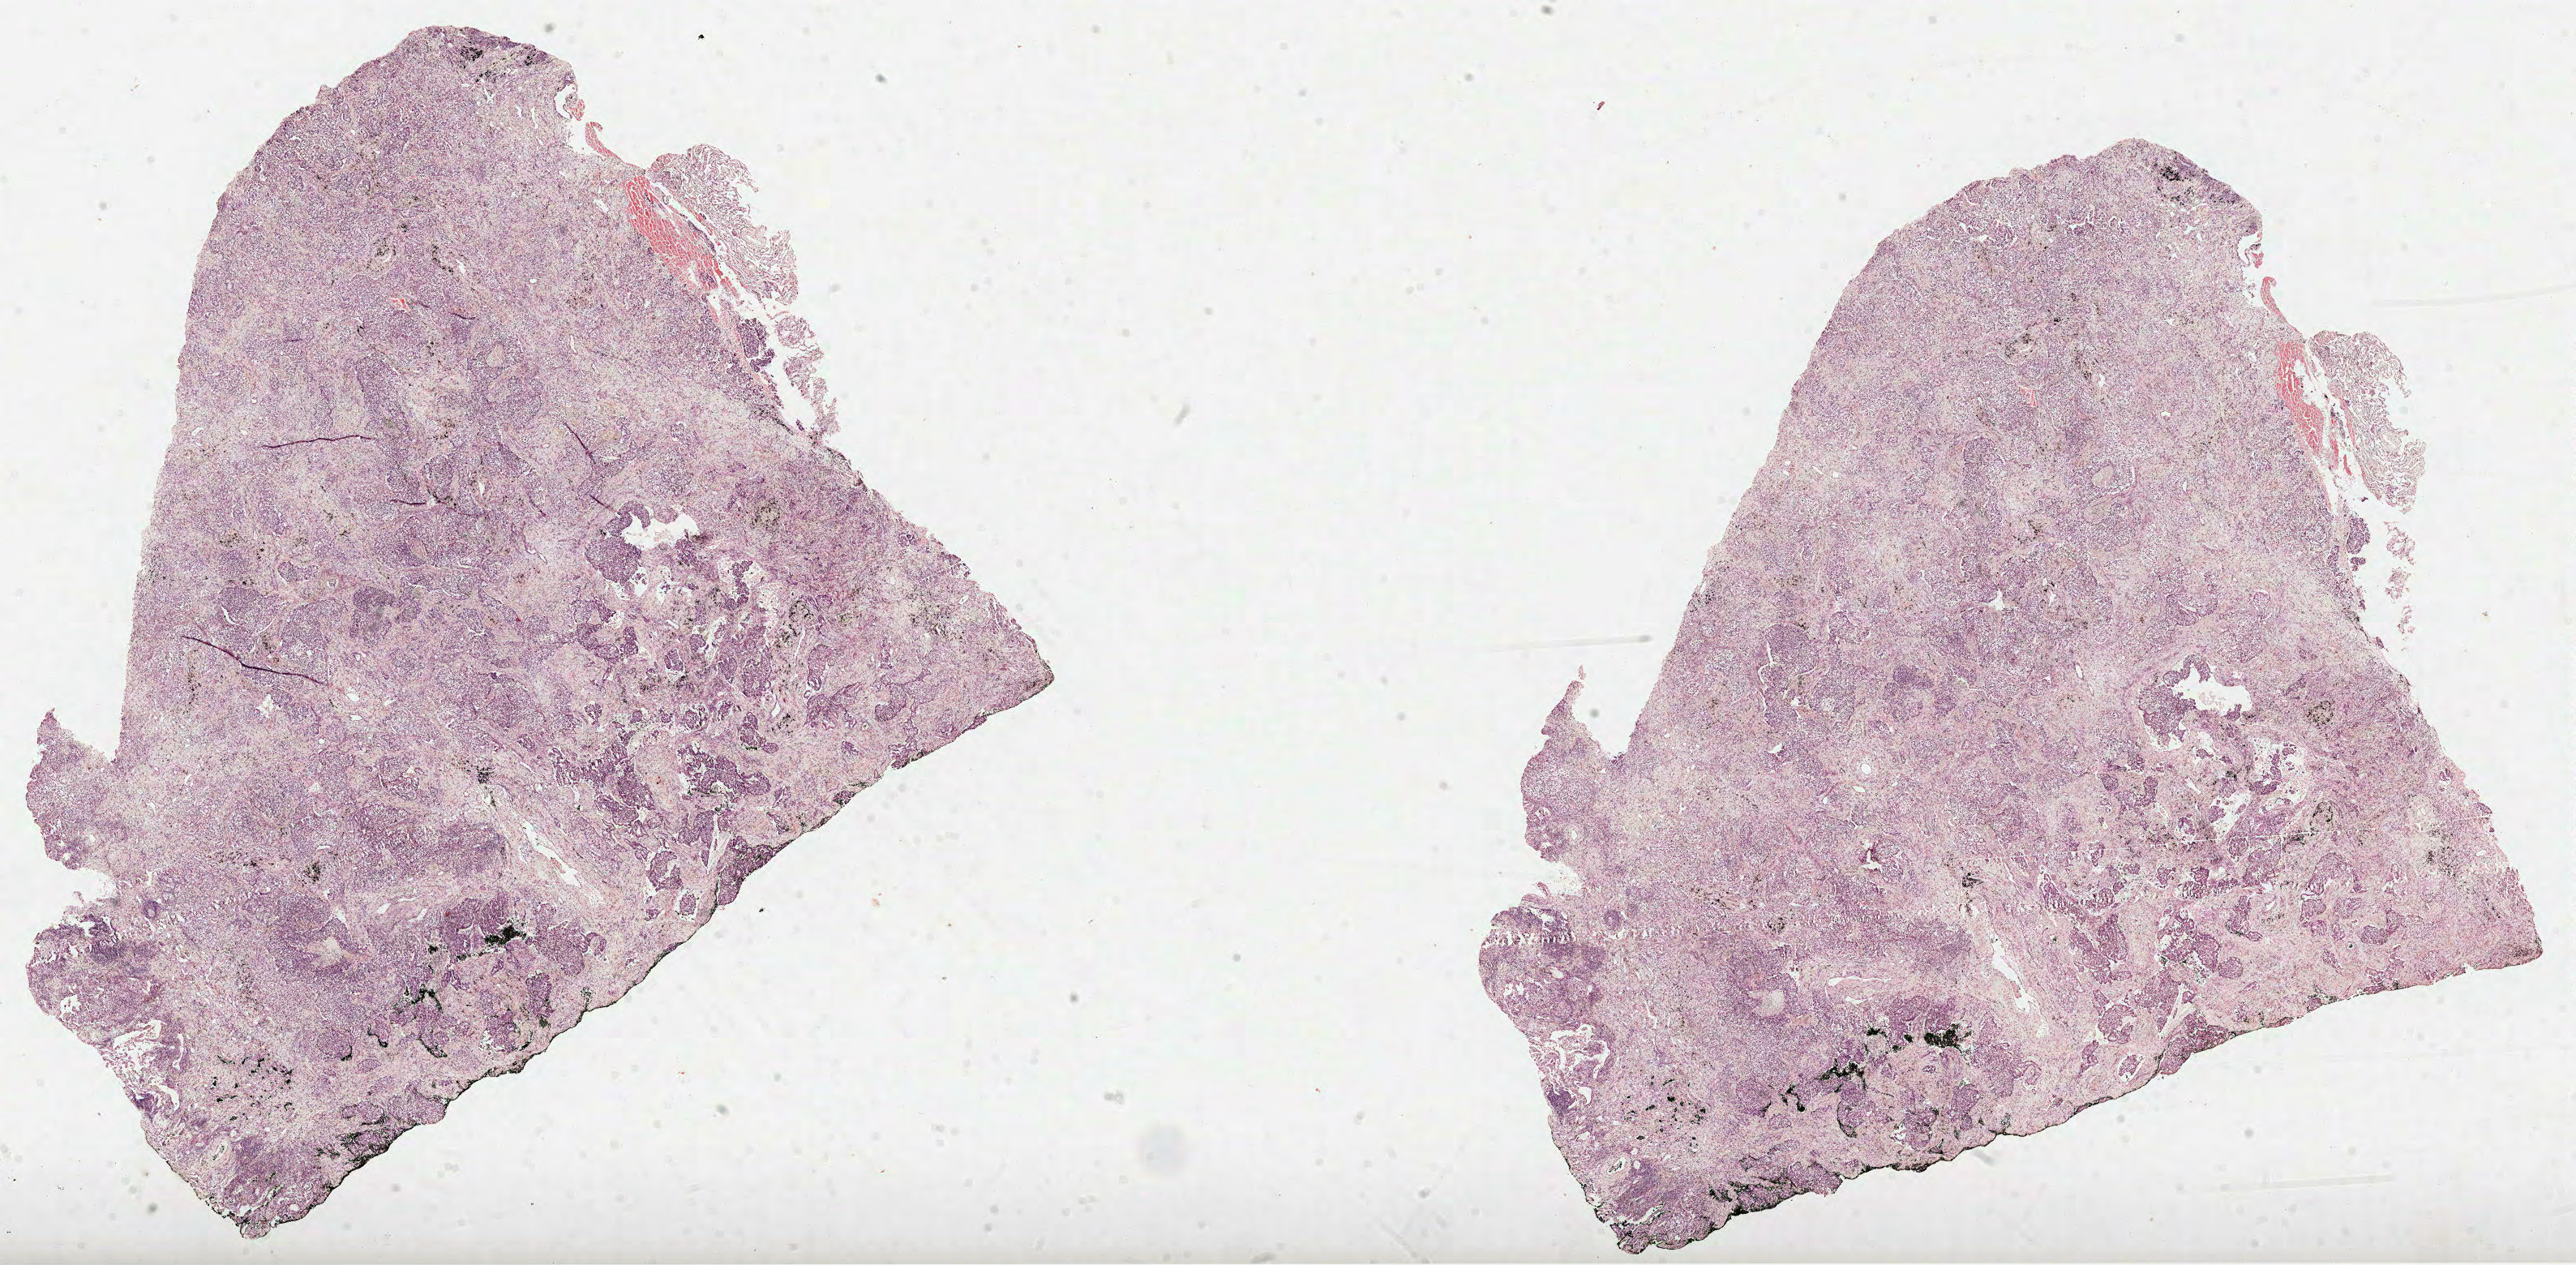
Hematoxylin and eosin (H&E) stained whole-slide image, low-resolution overview of the scanned area, about 25.6 x 12.6 mm (slide scanned at 40x); formalin-fixed paraffin-embedded (FFPE) diagnostic section; sample: primary tumour, lung. Female patient; age at initial diagnosis 74 years.
AJCC pathologic stage: IA (6th edition). Diagnosis: Clear cell adenocarcinoma, NOS (lower lobe, lung).